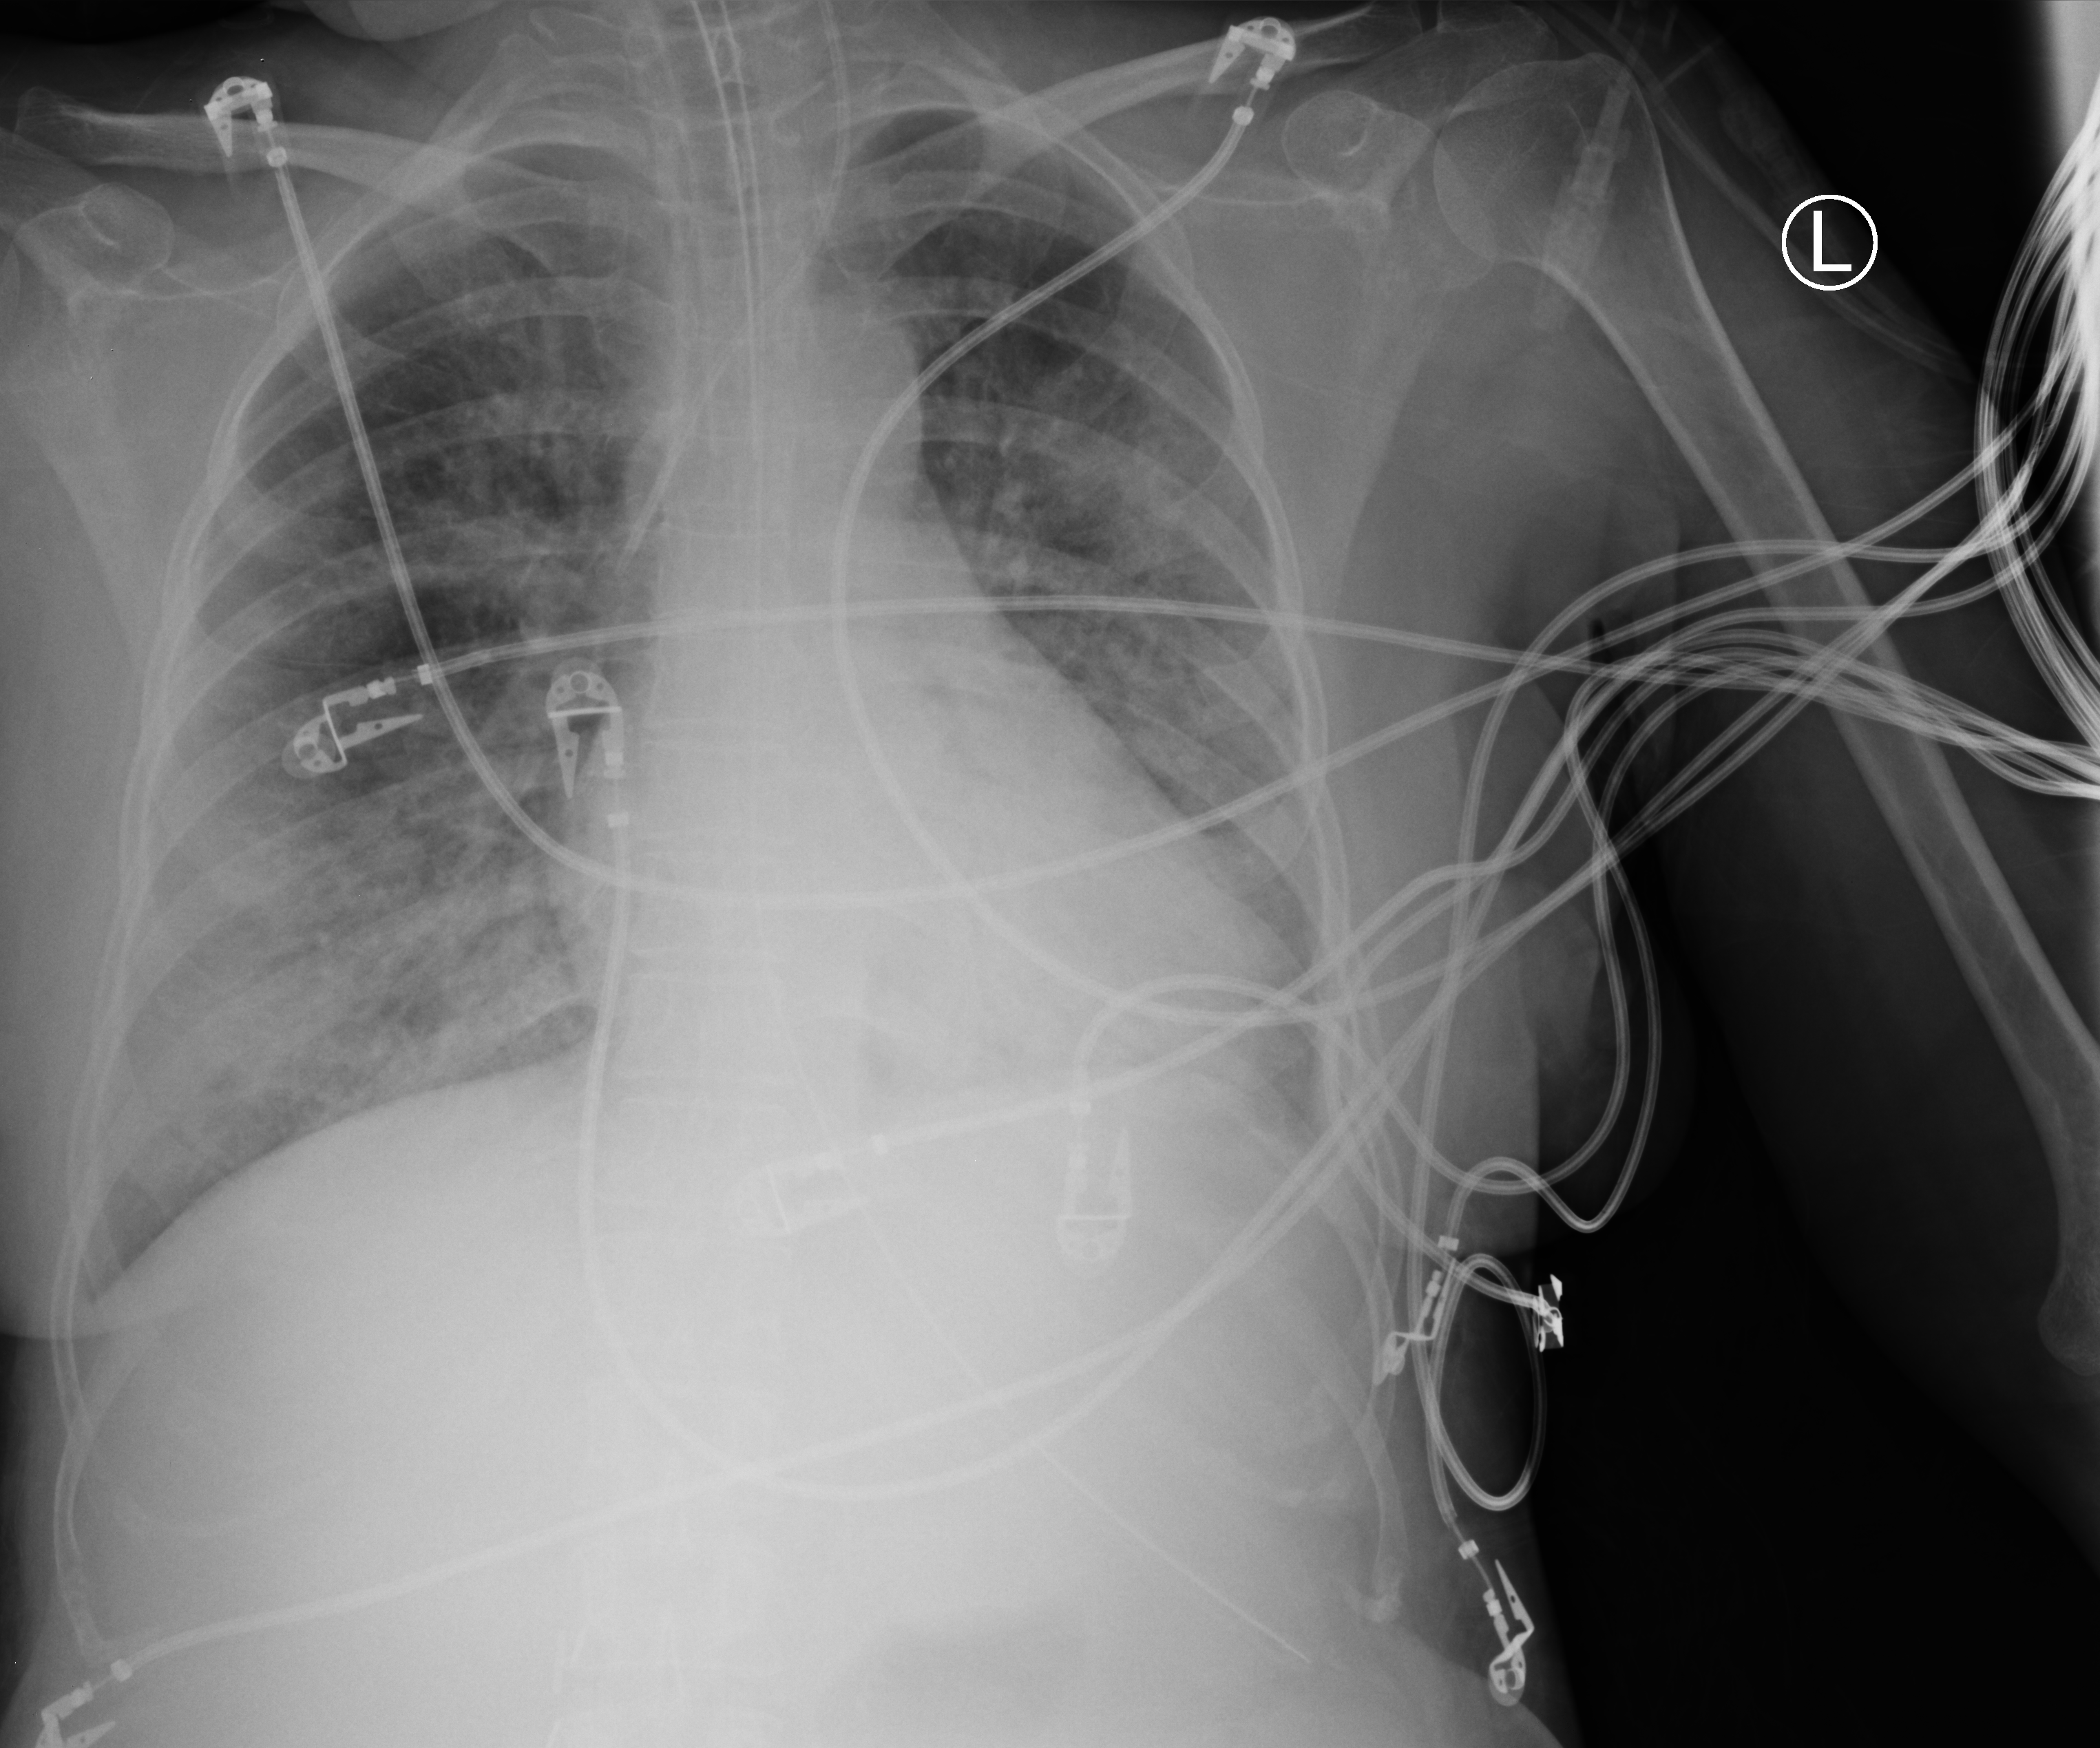
Bedside chest radiograph (computed radiography), anteroposterior (AP) projection. Patient hospitalised with COVID-19, aged 18–59 years.
From the hospital-stay record, not from the radiograph (when in the stay this image was taken is not recorded): mechanically ventilated during this hospital stay: yes; length of hospital stay: 10 days.